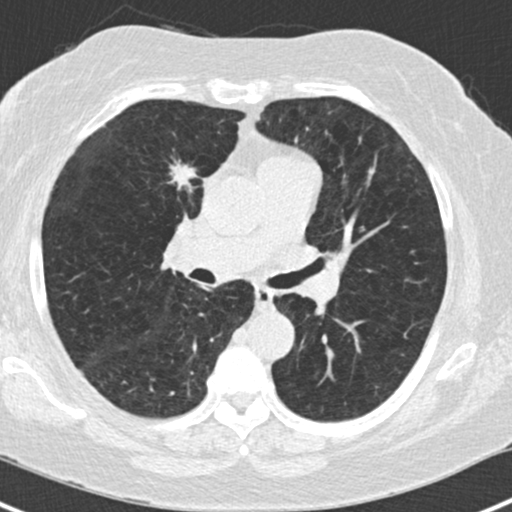
Low-dose screening chest CT, one axial slice. 120 kVp. Lung window (W 1500 / L -600 HU). 2 mm slice thickness. 512 × 512 image matrix.
Annotated regions visible in this slice (outlined manually by an expert reader):
- lesion 1 (tumor, upper lobe of right lung): bounding box (x1, y1, x2, y2) in pixels: (170, 160, 197, 192)